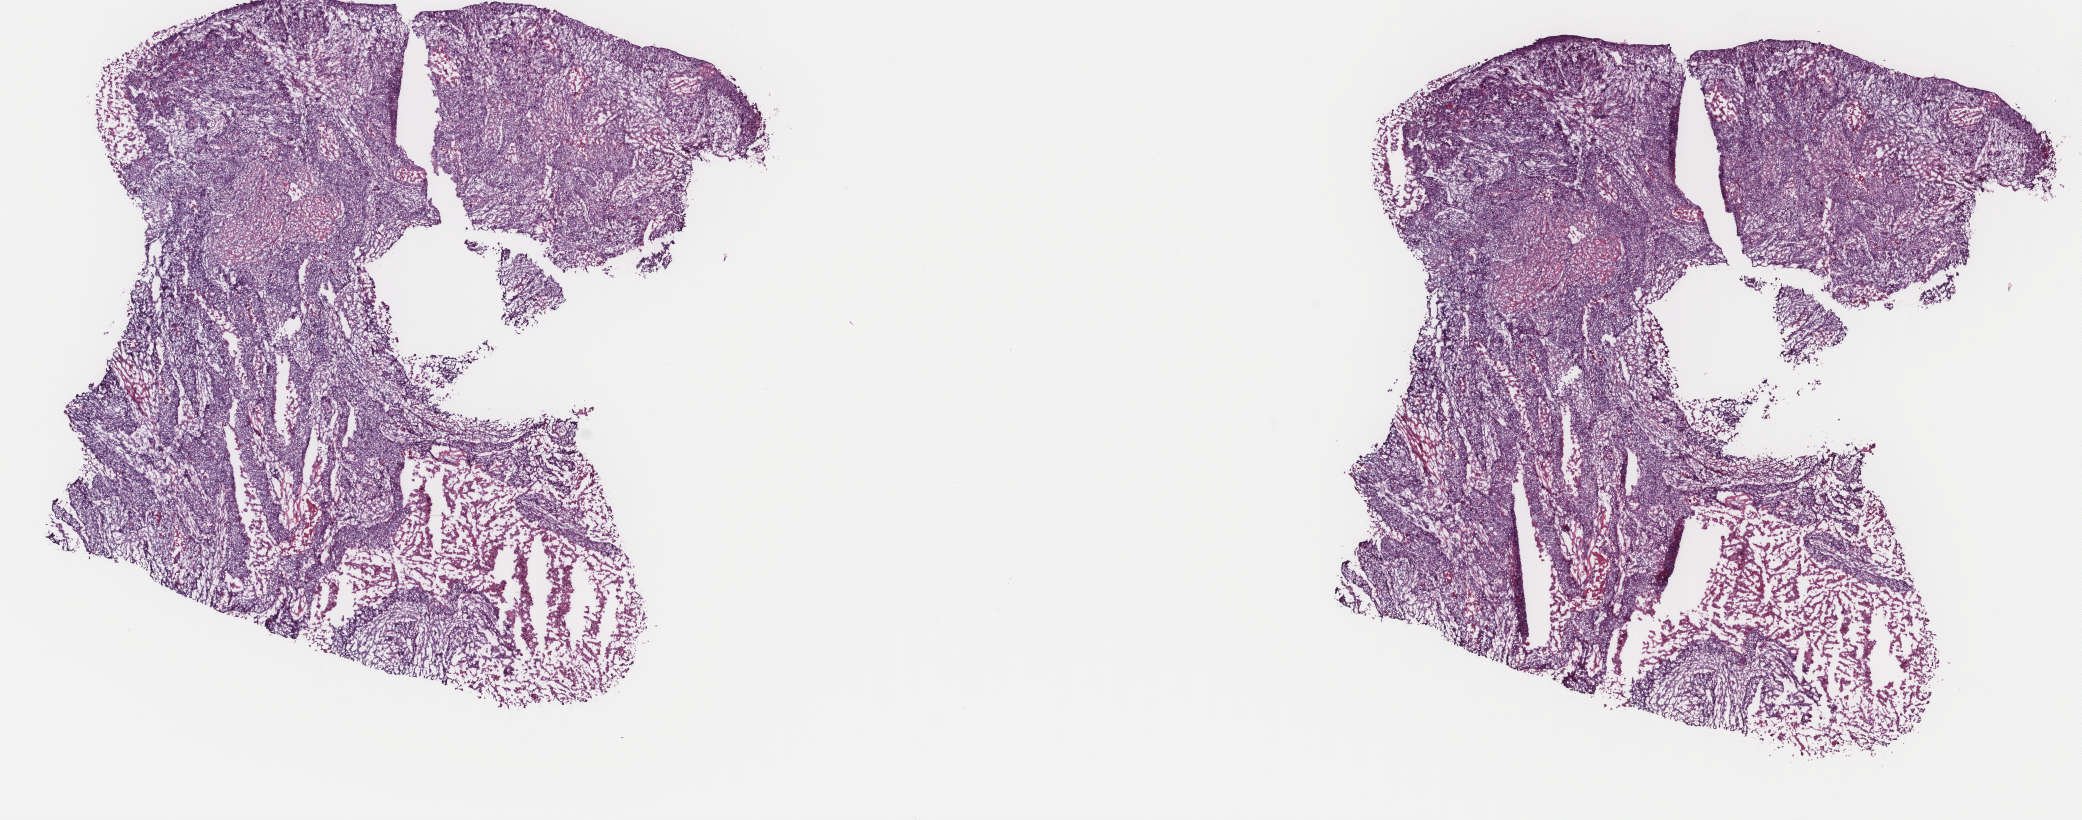
Digitized H&E-stained tissue section (whole slide), shown as a low-resolution overview of the whole scanned area (about 16.5 x 6.5 mm, slide scanned at 40x), frozen section, sample: primary tumour, bladder. Patient: male, age at initial diagnosis 85 years. Histologic grade: high grade. Slide review estimates, as recorded: tumour cells 55%, tumour nuclei 75%, normal cells 0%, stromal cells 25%, necrosis 20%. Inflammatory infiltration, as recorded: lymphocyte infiltration 2%, monocyte infiltration 0%, neutrophil infiltration 0%.
- AJCC pathologic stage: II
- diagnosis: Transitional cell carcinoma